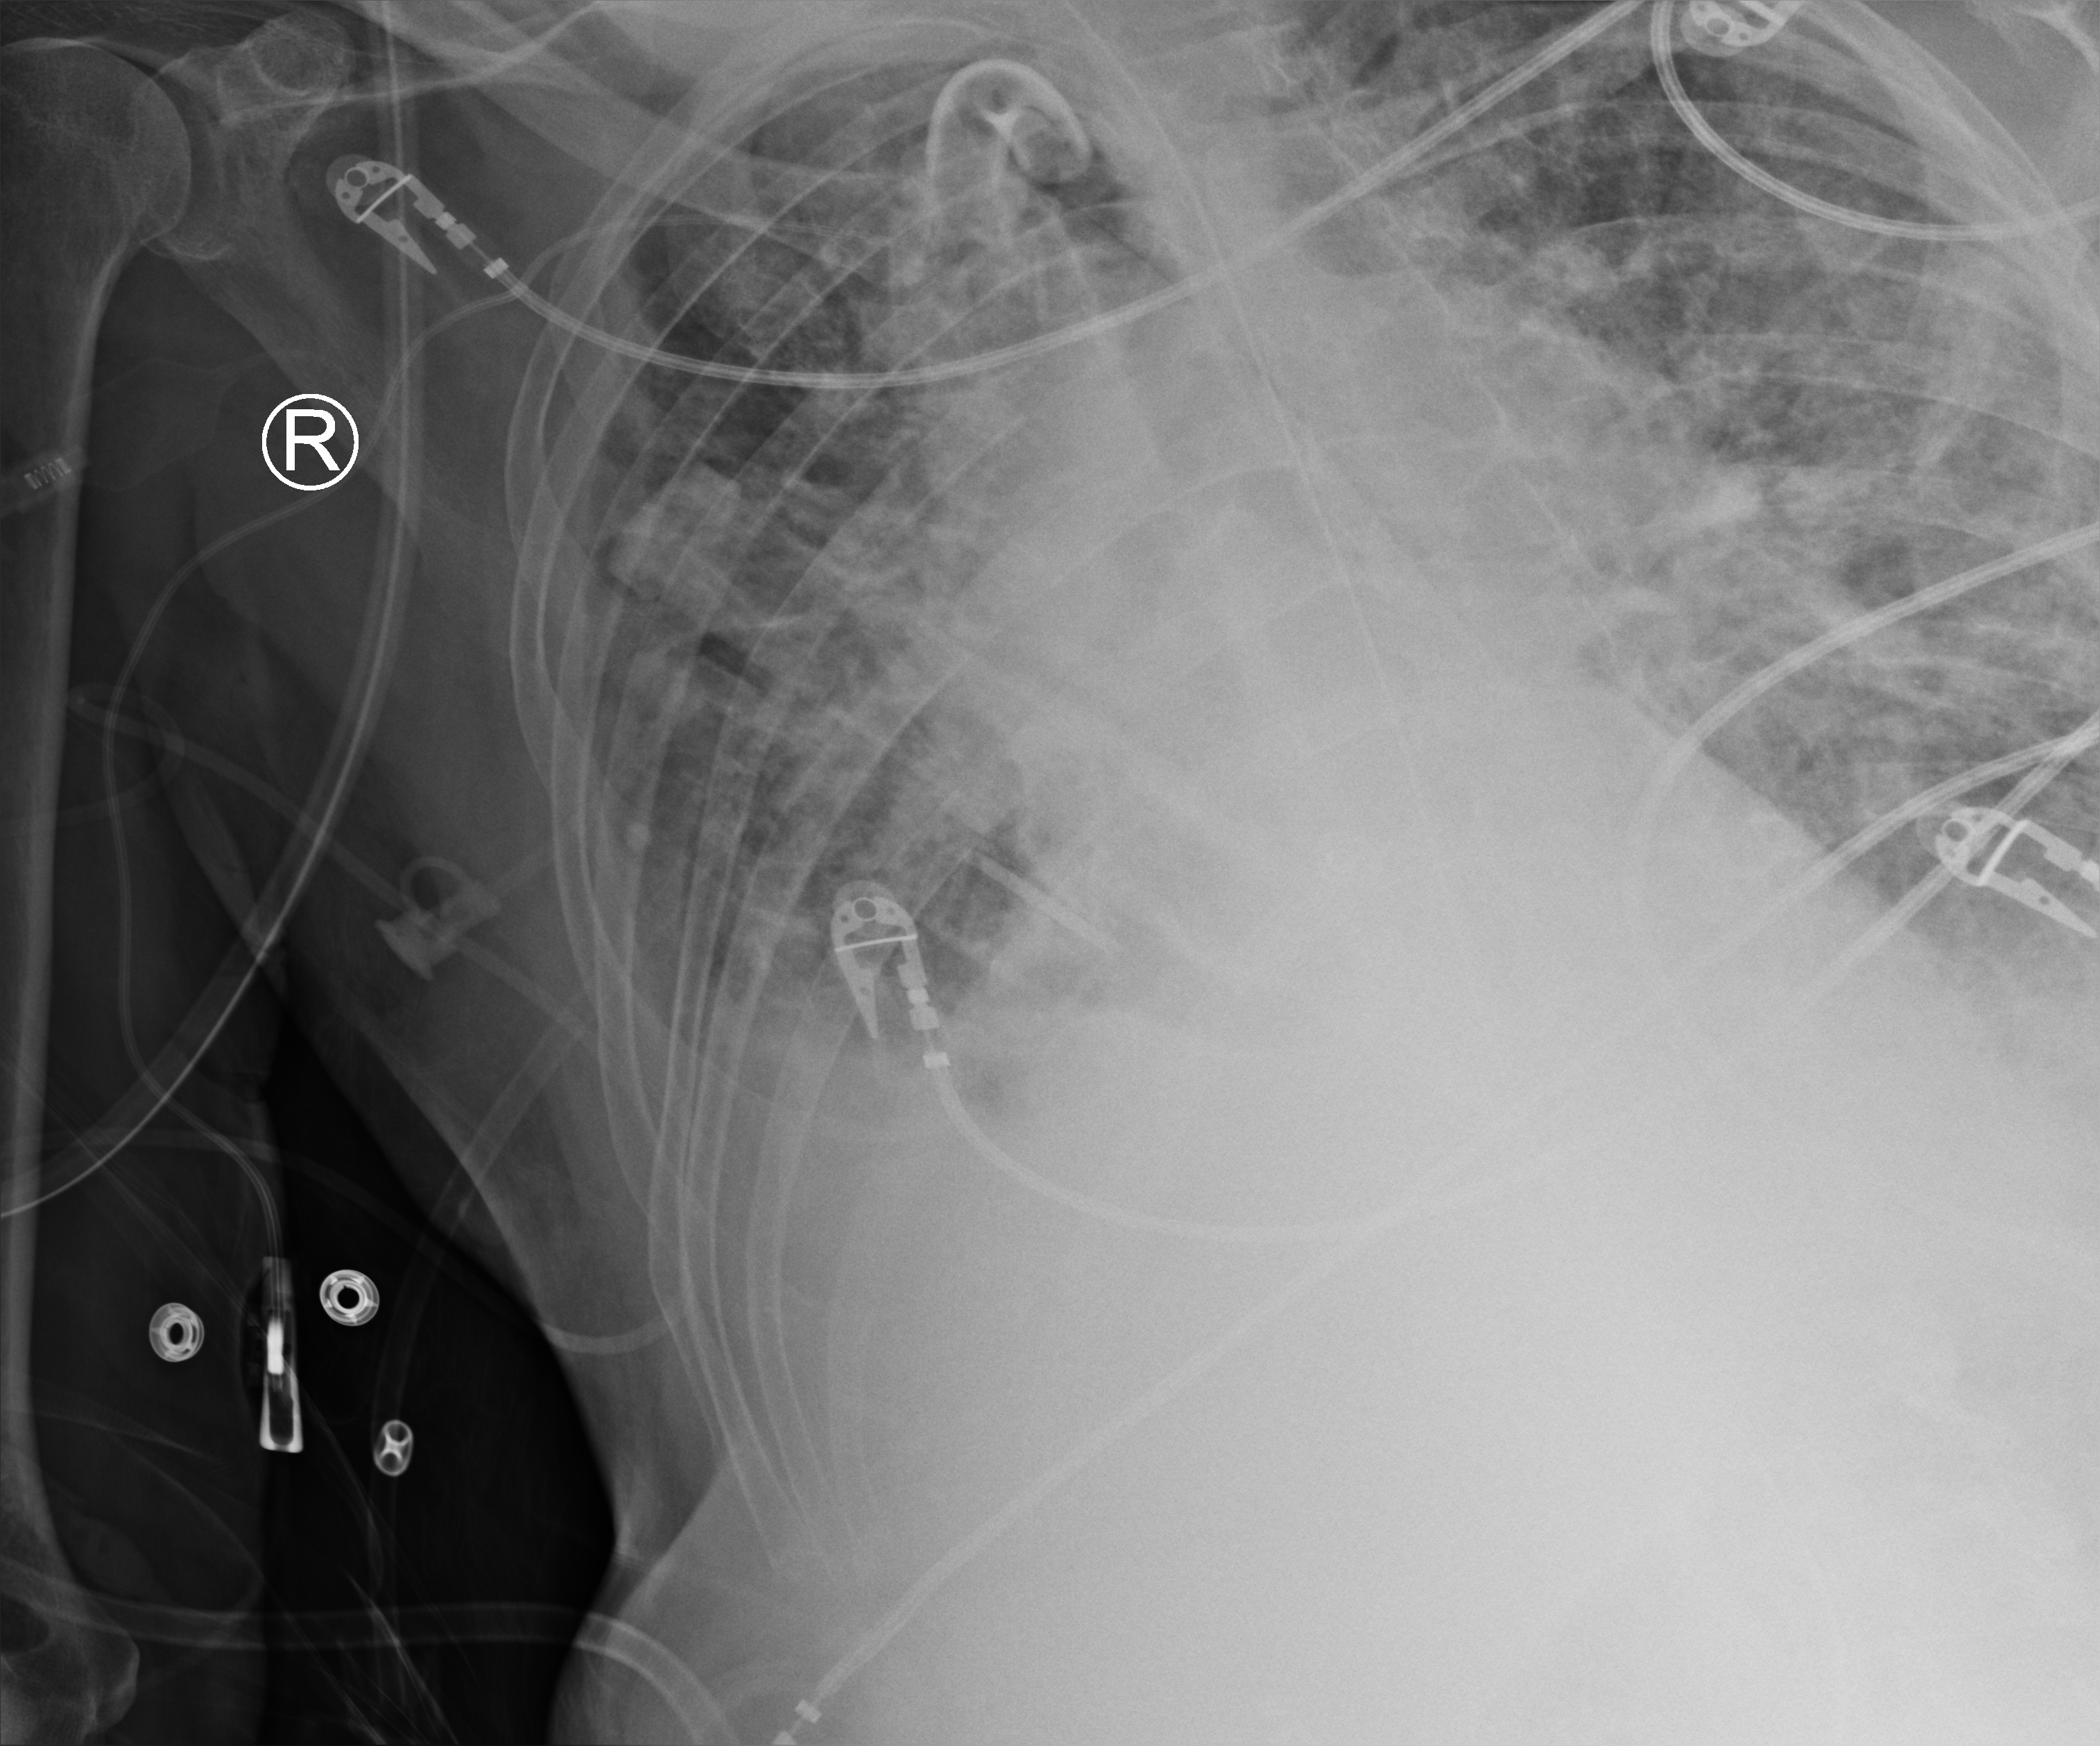
Bedside chest radiograph (computed radiography); anteroposterior (AP) projection. Male patient hospitalised with COVID-19, age 75–90 years.
Admission-level facts for this patient (not findings on this image; timing relative to this image not recorded): admitted to intensive care during this hospital stay: yes; mechanically ventilated during this hospital stay: yes.